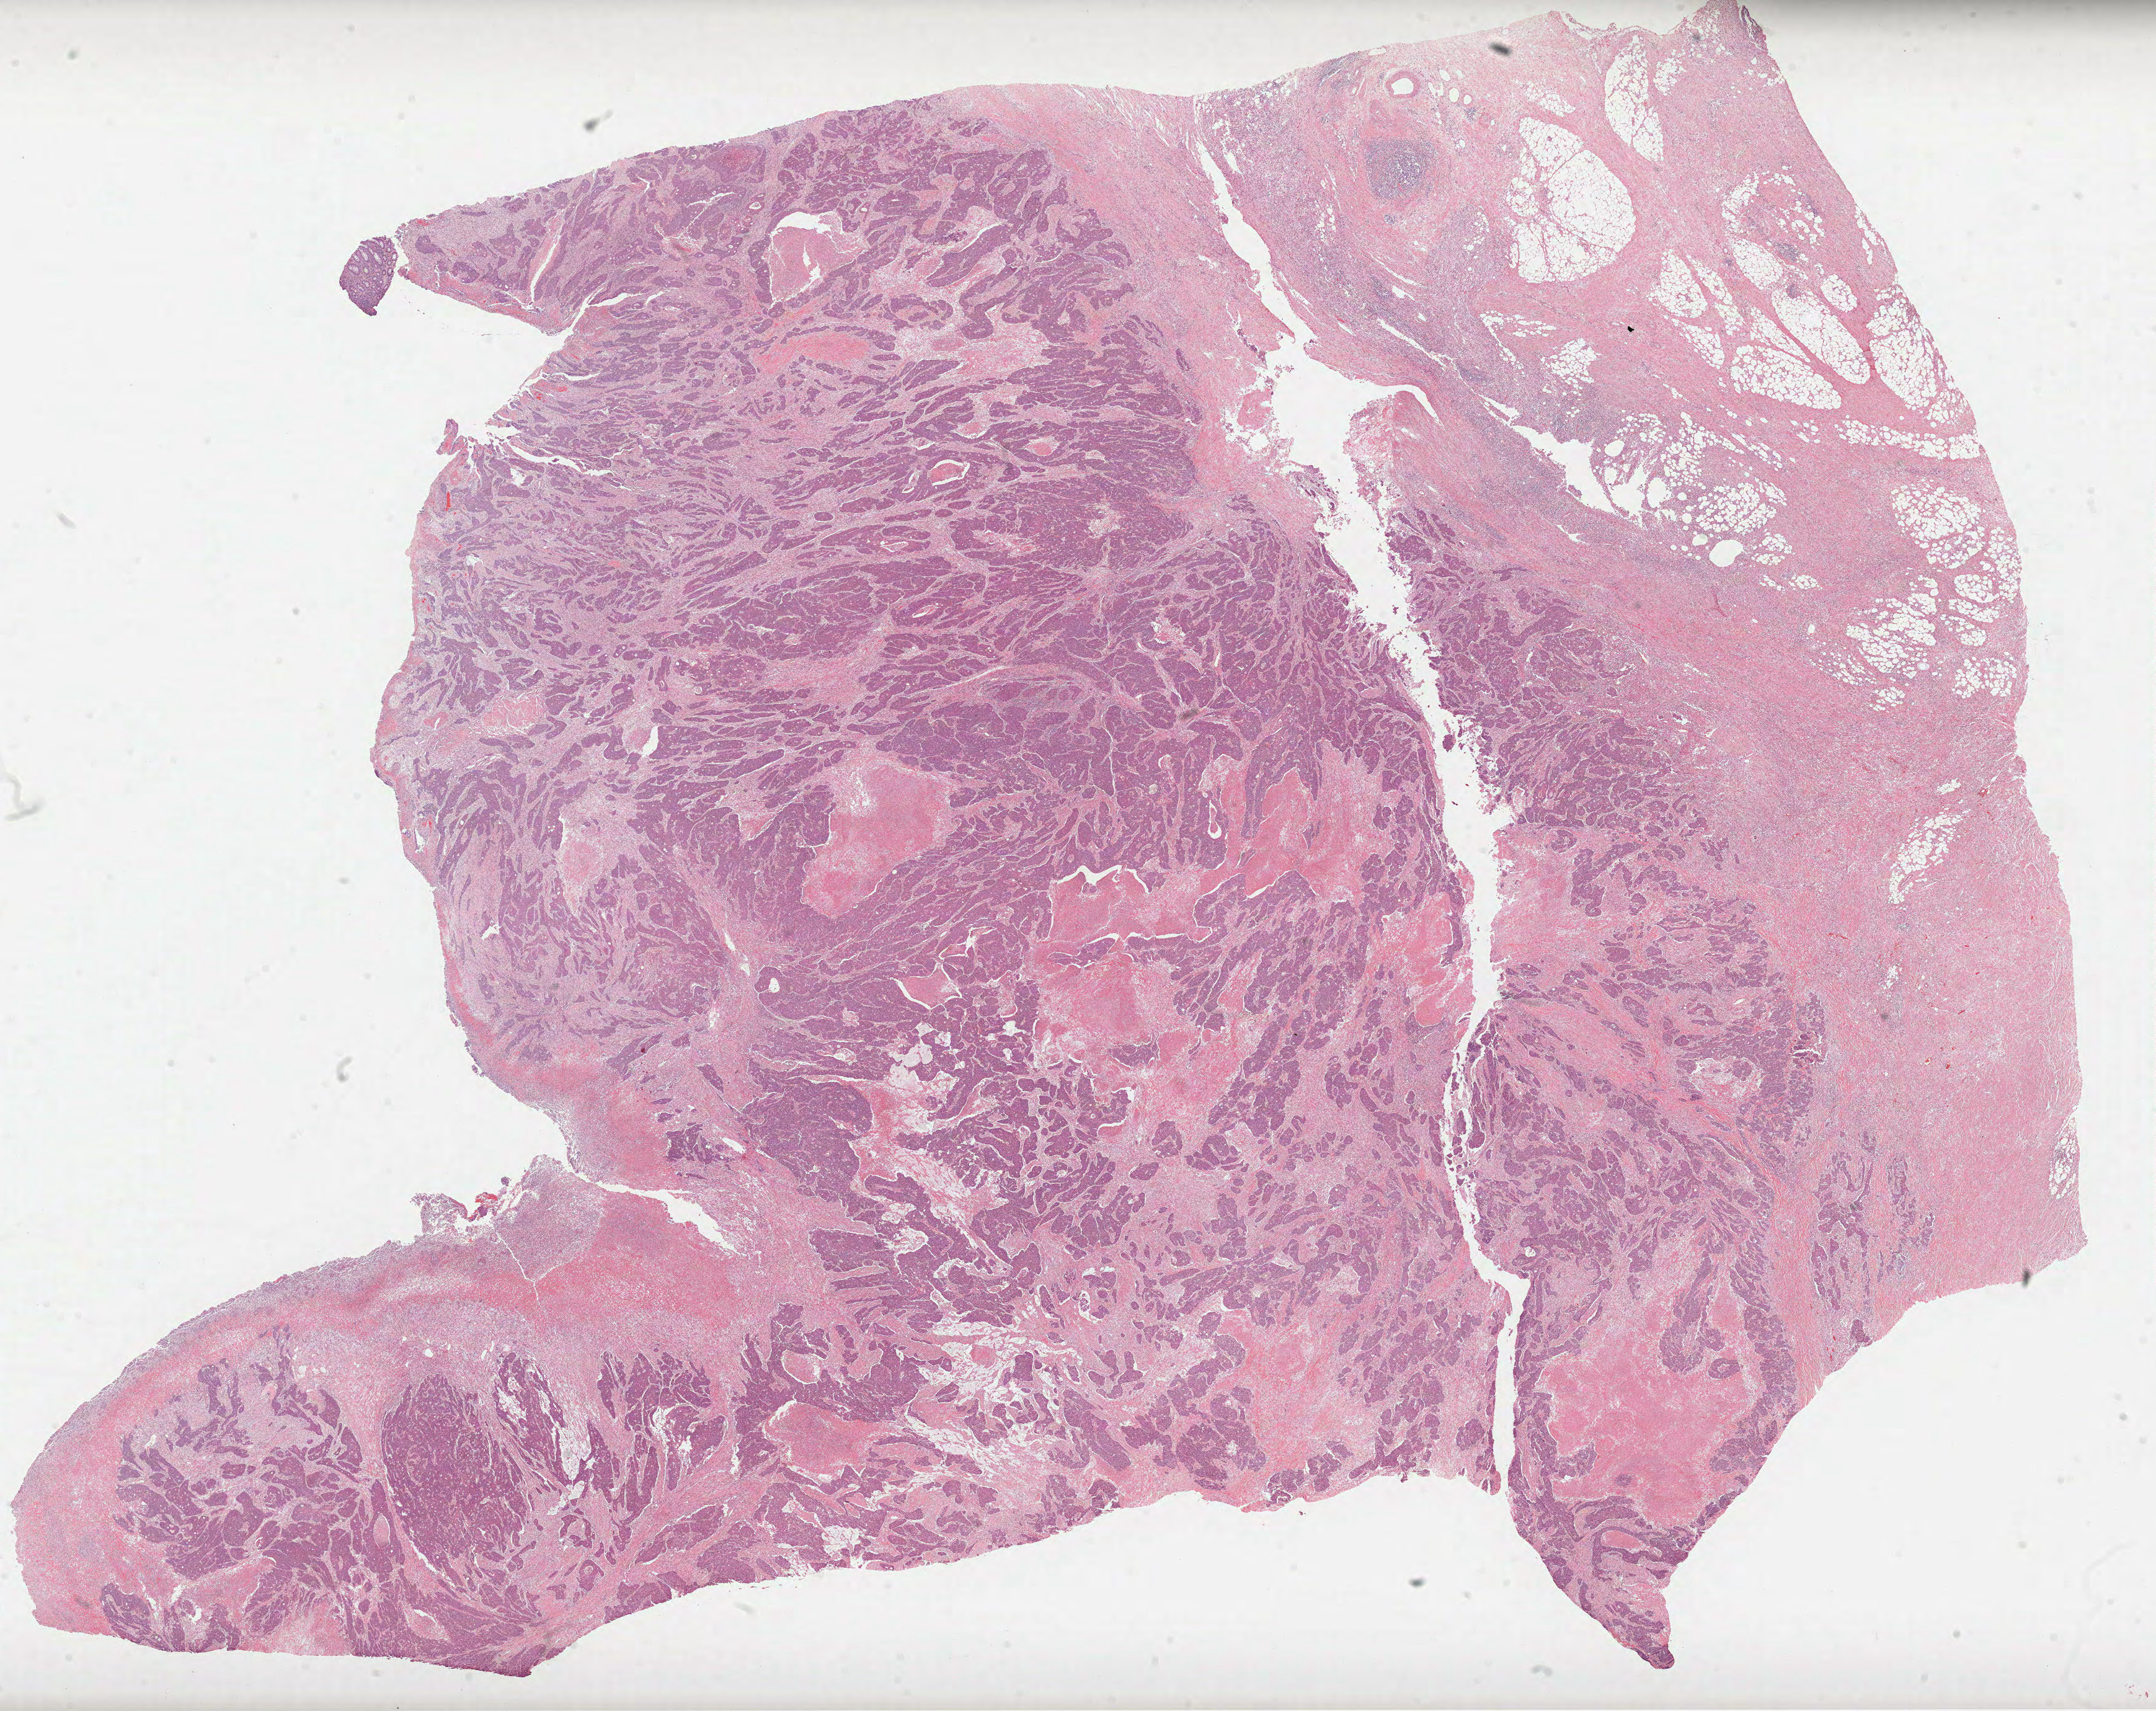
Whole-slide histology image, H&E — shown as a low-resolution overview of the whole scanned area (about 28.0 x 22.3 mm, slide scanned at 40x); formalin-fixed paraffin-embedded (FFPE) diagnostic section; sample: primary tumour, colon. Female patient; age at initial diagnosis 66 years.
AJCC pathologic stage: IIB (6th edition). TNM: T4 N0 M0. Pathologic diagnosis: Adenocarcinoma, NOS (transverse colon).